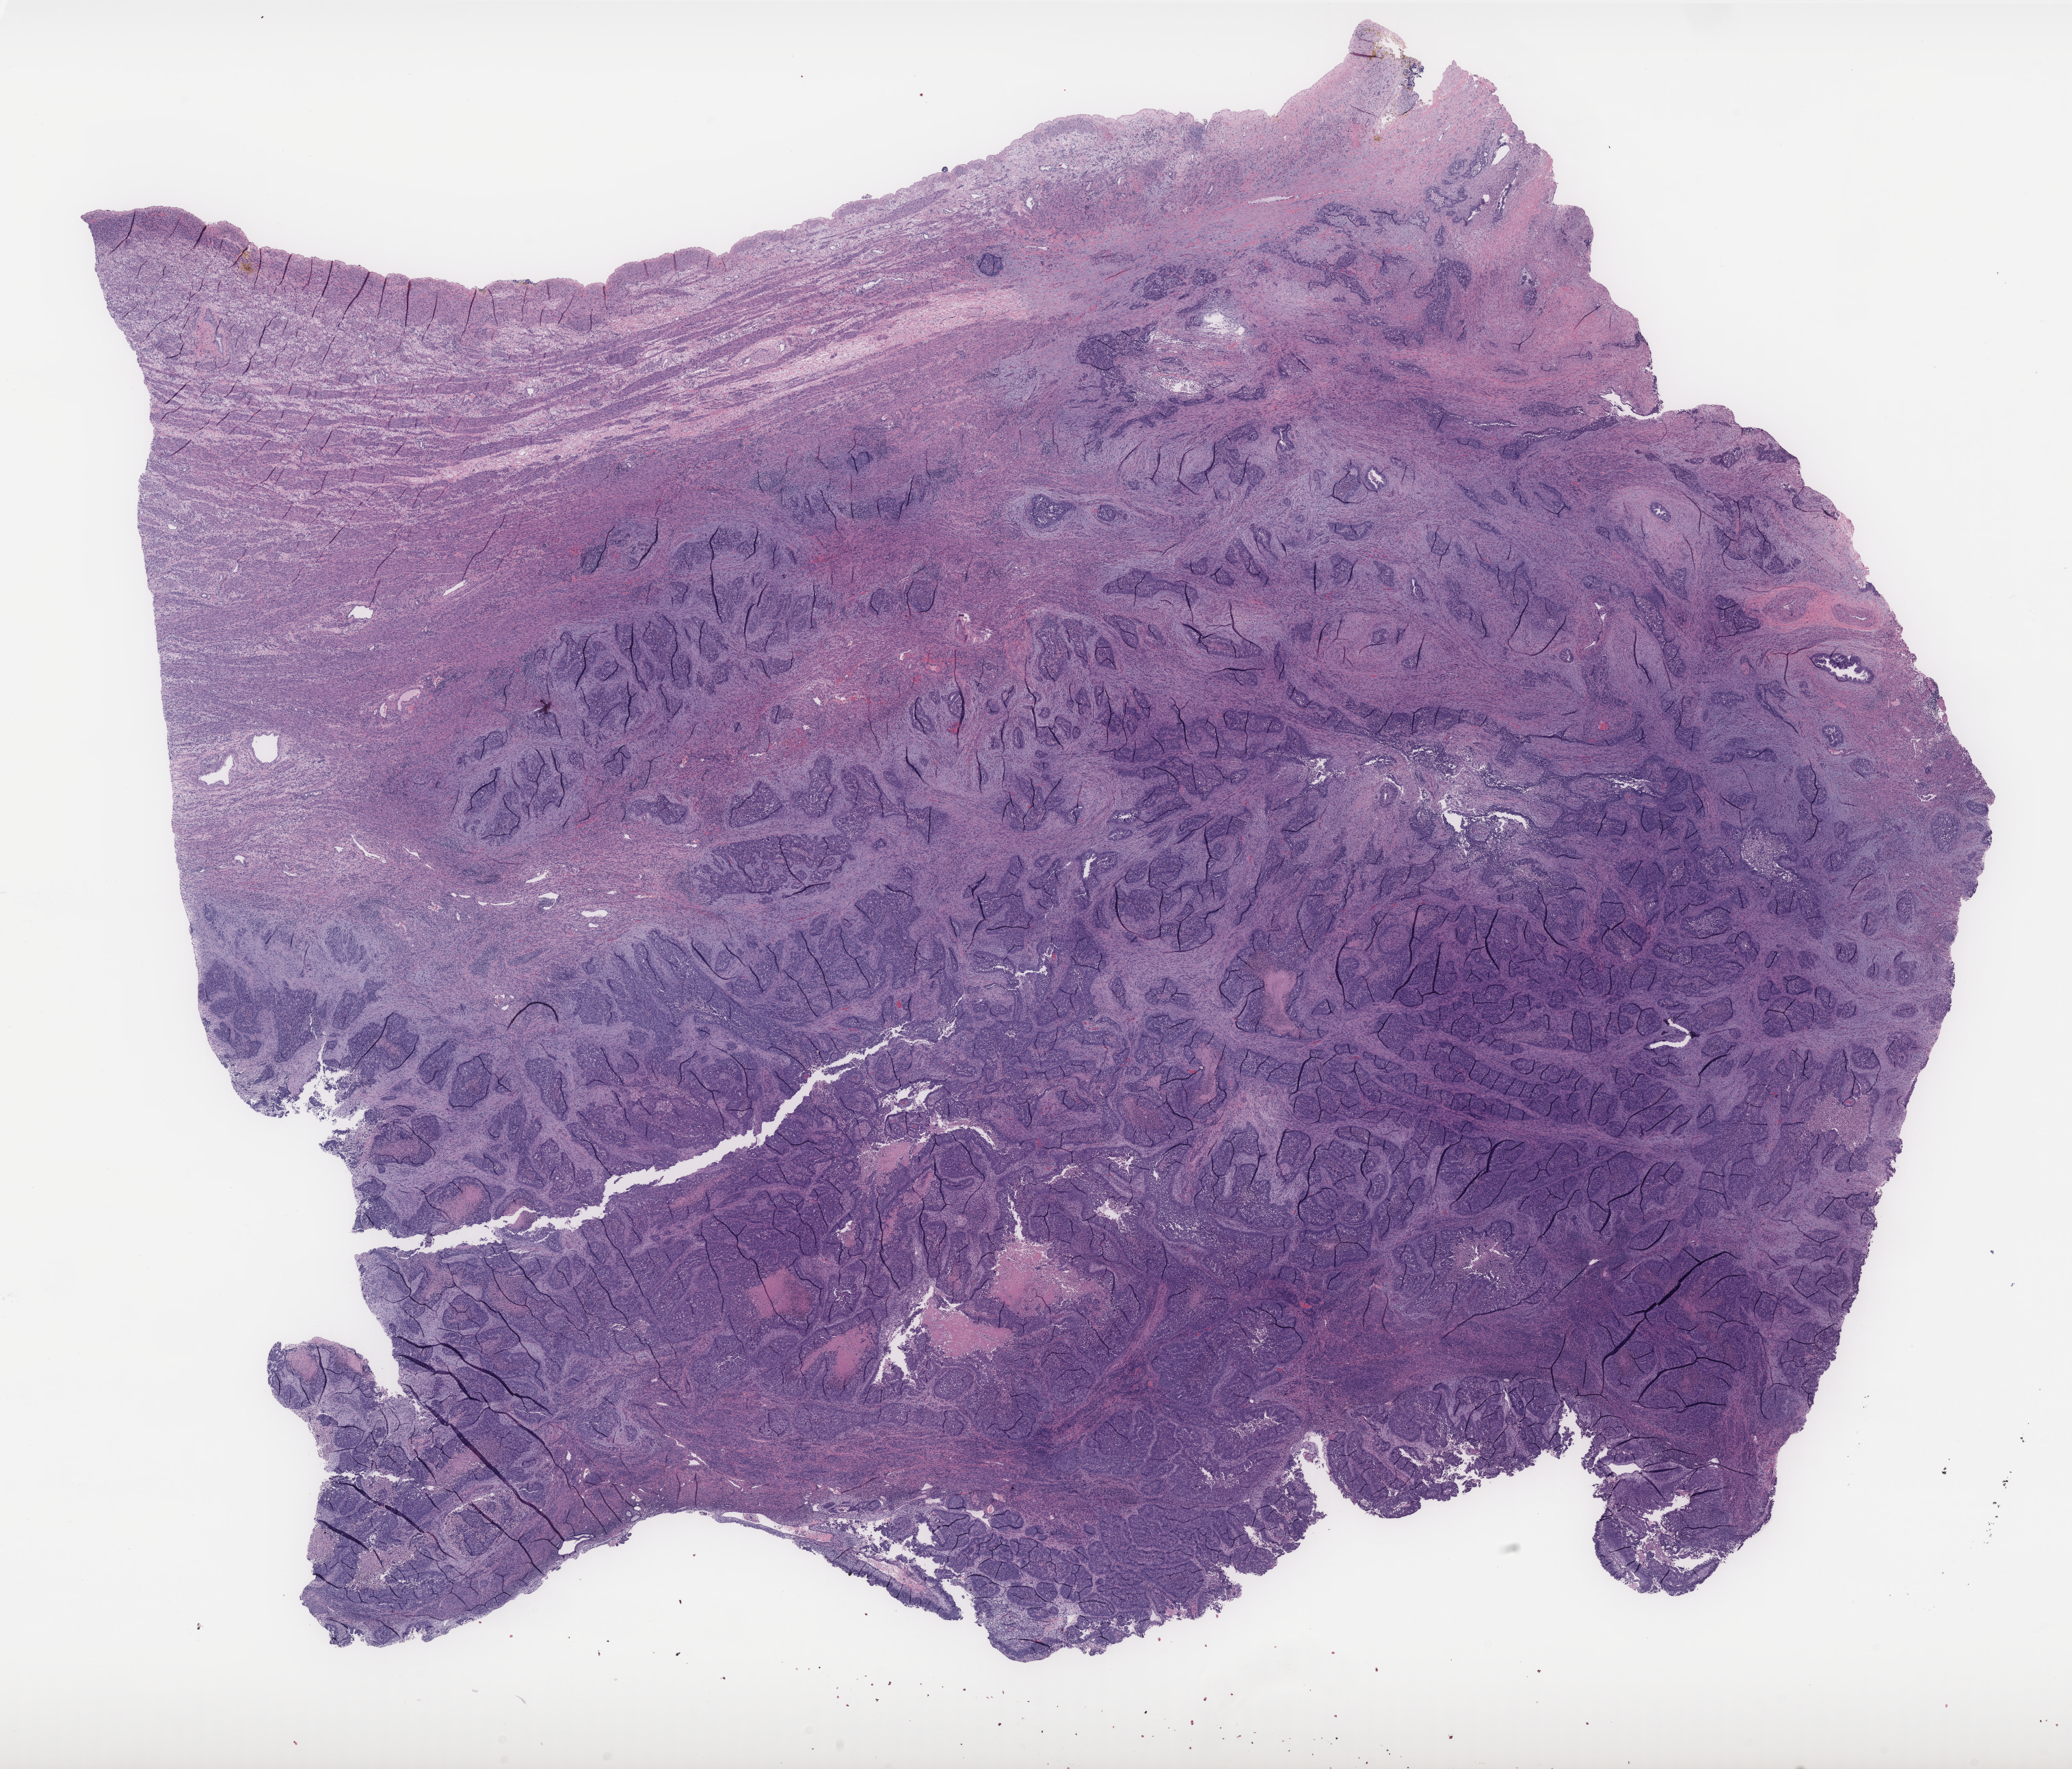
Digitized H&E-stained tissue section (whole slide), whole scanned area (about 24.3 x 20.7 mm, from a 40x scan) shown as a low-resolution overview, formalin-fixed paraffin-embedded (FFPE) diagnostic section, uterus, primary tumour sample. Patient: female, age at initial diagnosis 73 years. Histologic grade: G3 (poorly differentiated).
* FIGO stage: IIIC2
* histologic diagnosis: Serous cystadenocarcinoma, NOS (endometrium)
* lymph nodes positive (case pathology): 3 of 5 examined